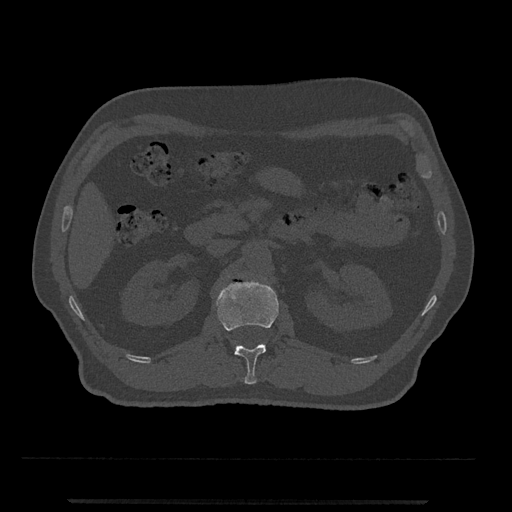
CT including the spine, one axial slice; position 319 of 797 along the scan axis; reconstruction kernel Br40s/3; 120 kVp; bone window (W 1800 / L 400 HU); 0.5 mm slice thickness; 512 × 512 image matrix, field of view 419 × 419 mm. Patient: male, 63 years. Case-level facts recorded for this patient, not image findings: primary cancer: prostate.
Outlined on this slice (semi-automatically segmented with operator editing):
- L1 vertebra: bounding box (x1, y1, x2, y2) in pixels: (216, 280, 279, 385)